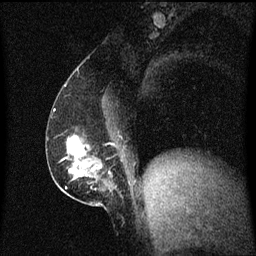
Breast MRI (dynamic contrast-enhanced), one sagittal slice. Slice 28 of 60 in the series (ordered by position). Dynamic contrast-enhanced series, image 2 of 3 at this slice position (ordered by acquisition). 1.5 T. TE 4.2 ms, TR 8.4 ms. 2 mm slice thickness. 256 × 256 image matrix, field of view 200 × 200 mm. Patient: female, 52 years. From the clinical record (not read from this slice): setting: breast cancer imaged before/during neoadjuvant chemotherapy; receptor status: HER2-positive.
Outlined on this slice (semi-automatically segmented with operator editing):
- analysis volume of interest (the breast-tissue region the enhancement analysis was run in; not a lesion): box from (x=62, y=134) to (x=120, y=203) px
- tumour enhancement mask (voxels above the 70 % enhancement threshold inside the analysis volume of interest): (x=68, y=136)–(x=87, y=167)